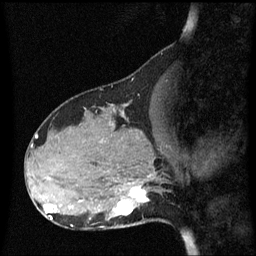
Breast MRI (dynamic contrast-enhanced), one sagittal slice; dynamic contrast-enhanced series, image 2 of 3 at this slice position (ordered by acquisition); 1.5 T; TE 4.2 ms, TR 8.4 ms; 2.1 mm slice thickness; 256 × 256 image matrix, field of view 210 × 210 mm. Patient: female, 31 years. From the clinical record (not read from this slice): setting: breast cancer imaged before/during neoadjuvant chemotherapy; receptor status: HR-positive, HER2-negative.
Annotated regions visible in this slice (semi-automatic segmentation, software-assisted and operator-edited):
- analysis volume of interest (the breast-tissue region the enhancement analysis was run in; not a lesion): bounding box [x1, y1, x2, y2] px = [98, 175, 164, 228]
- tumour enhancement mask (voxels above the 70 % enhancement threshold inside the analysis volume of interest): [118, 188, 149, 216]